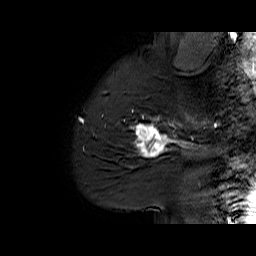
Breast MRI (dynamic contrast-enhanced), one sagittal slice; position 50 of 60 along the scan axis; dynamic contrast-enhanced series, time point 2 of 6 at this slice position (early post-contrast); 1.5 T; TE 6.1 ms, TR 32.9 ms; 256 × 256 image matrix, field of view 220 × 220 mm. Female patient. Case-level facts recorded for this patient, not image findings: setting: breast cancer imaged before/during neoadjuvant chemotherapy; receptor status: HER2-positive.
Annotated regions visible in this slice (semi-automatically segmented with operator editing):
- analysis volume of interest (the breast-tissue region the enhancement analysis was run in; not a lesion): bounding box [x1, y1, x2, y2] px = [127, 95, 194, 165]
- tumour enhancement mask (voxels above the 100 % enhancement threshold inside the analysis volume of interest): [134, 114, 194, 157]